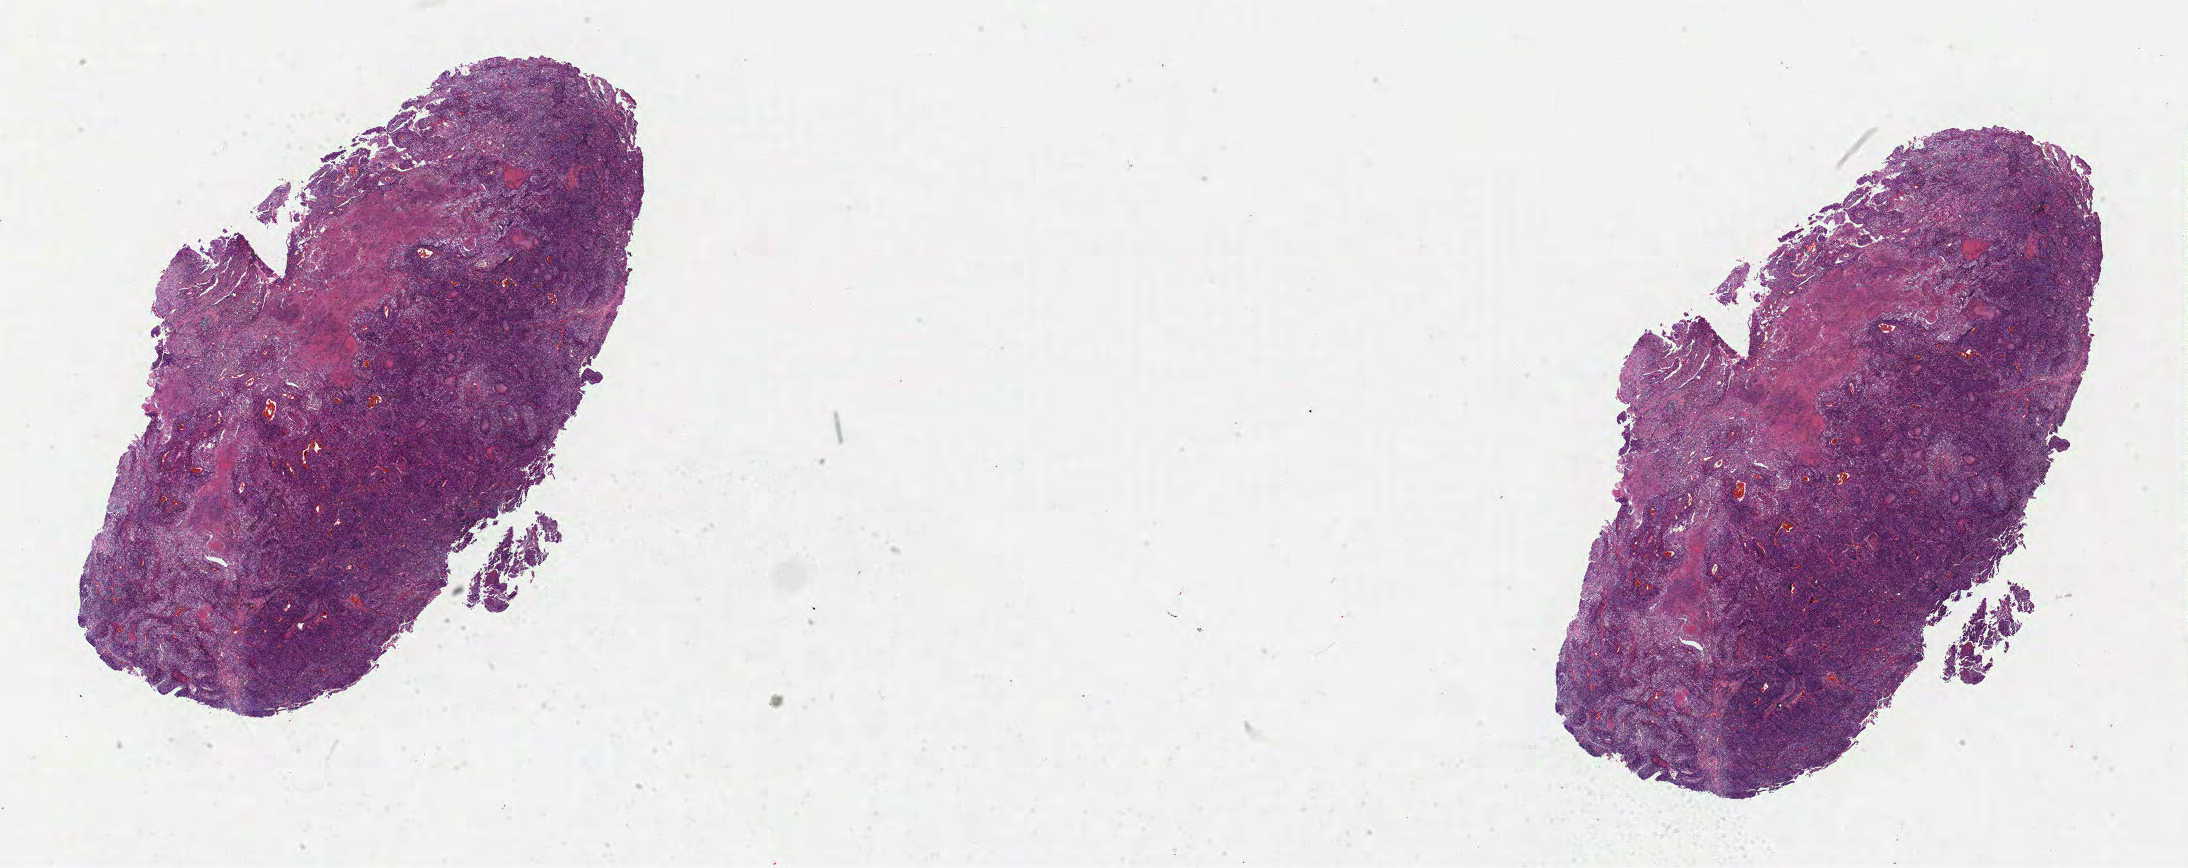
Whole-slide histology image, H&E — low-resolution overview of the scanned area, about 35.3 x 14.0 mm. Formalin-fixed paraffin-embedded (FFPE) diagnostic section. Primary tumour sample from the lung. Patient: male, age at initial diagnosis 38 years.
Histologic diagnosis: Adenocarcinoma, NOS (upper lobe, lung).